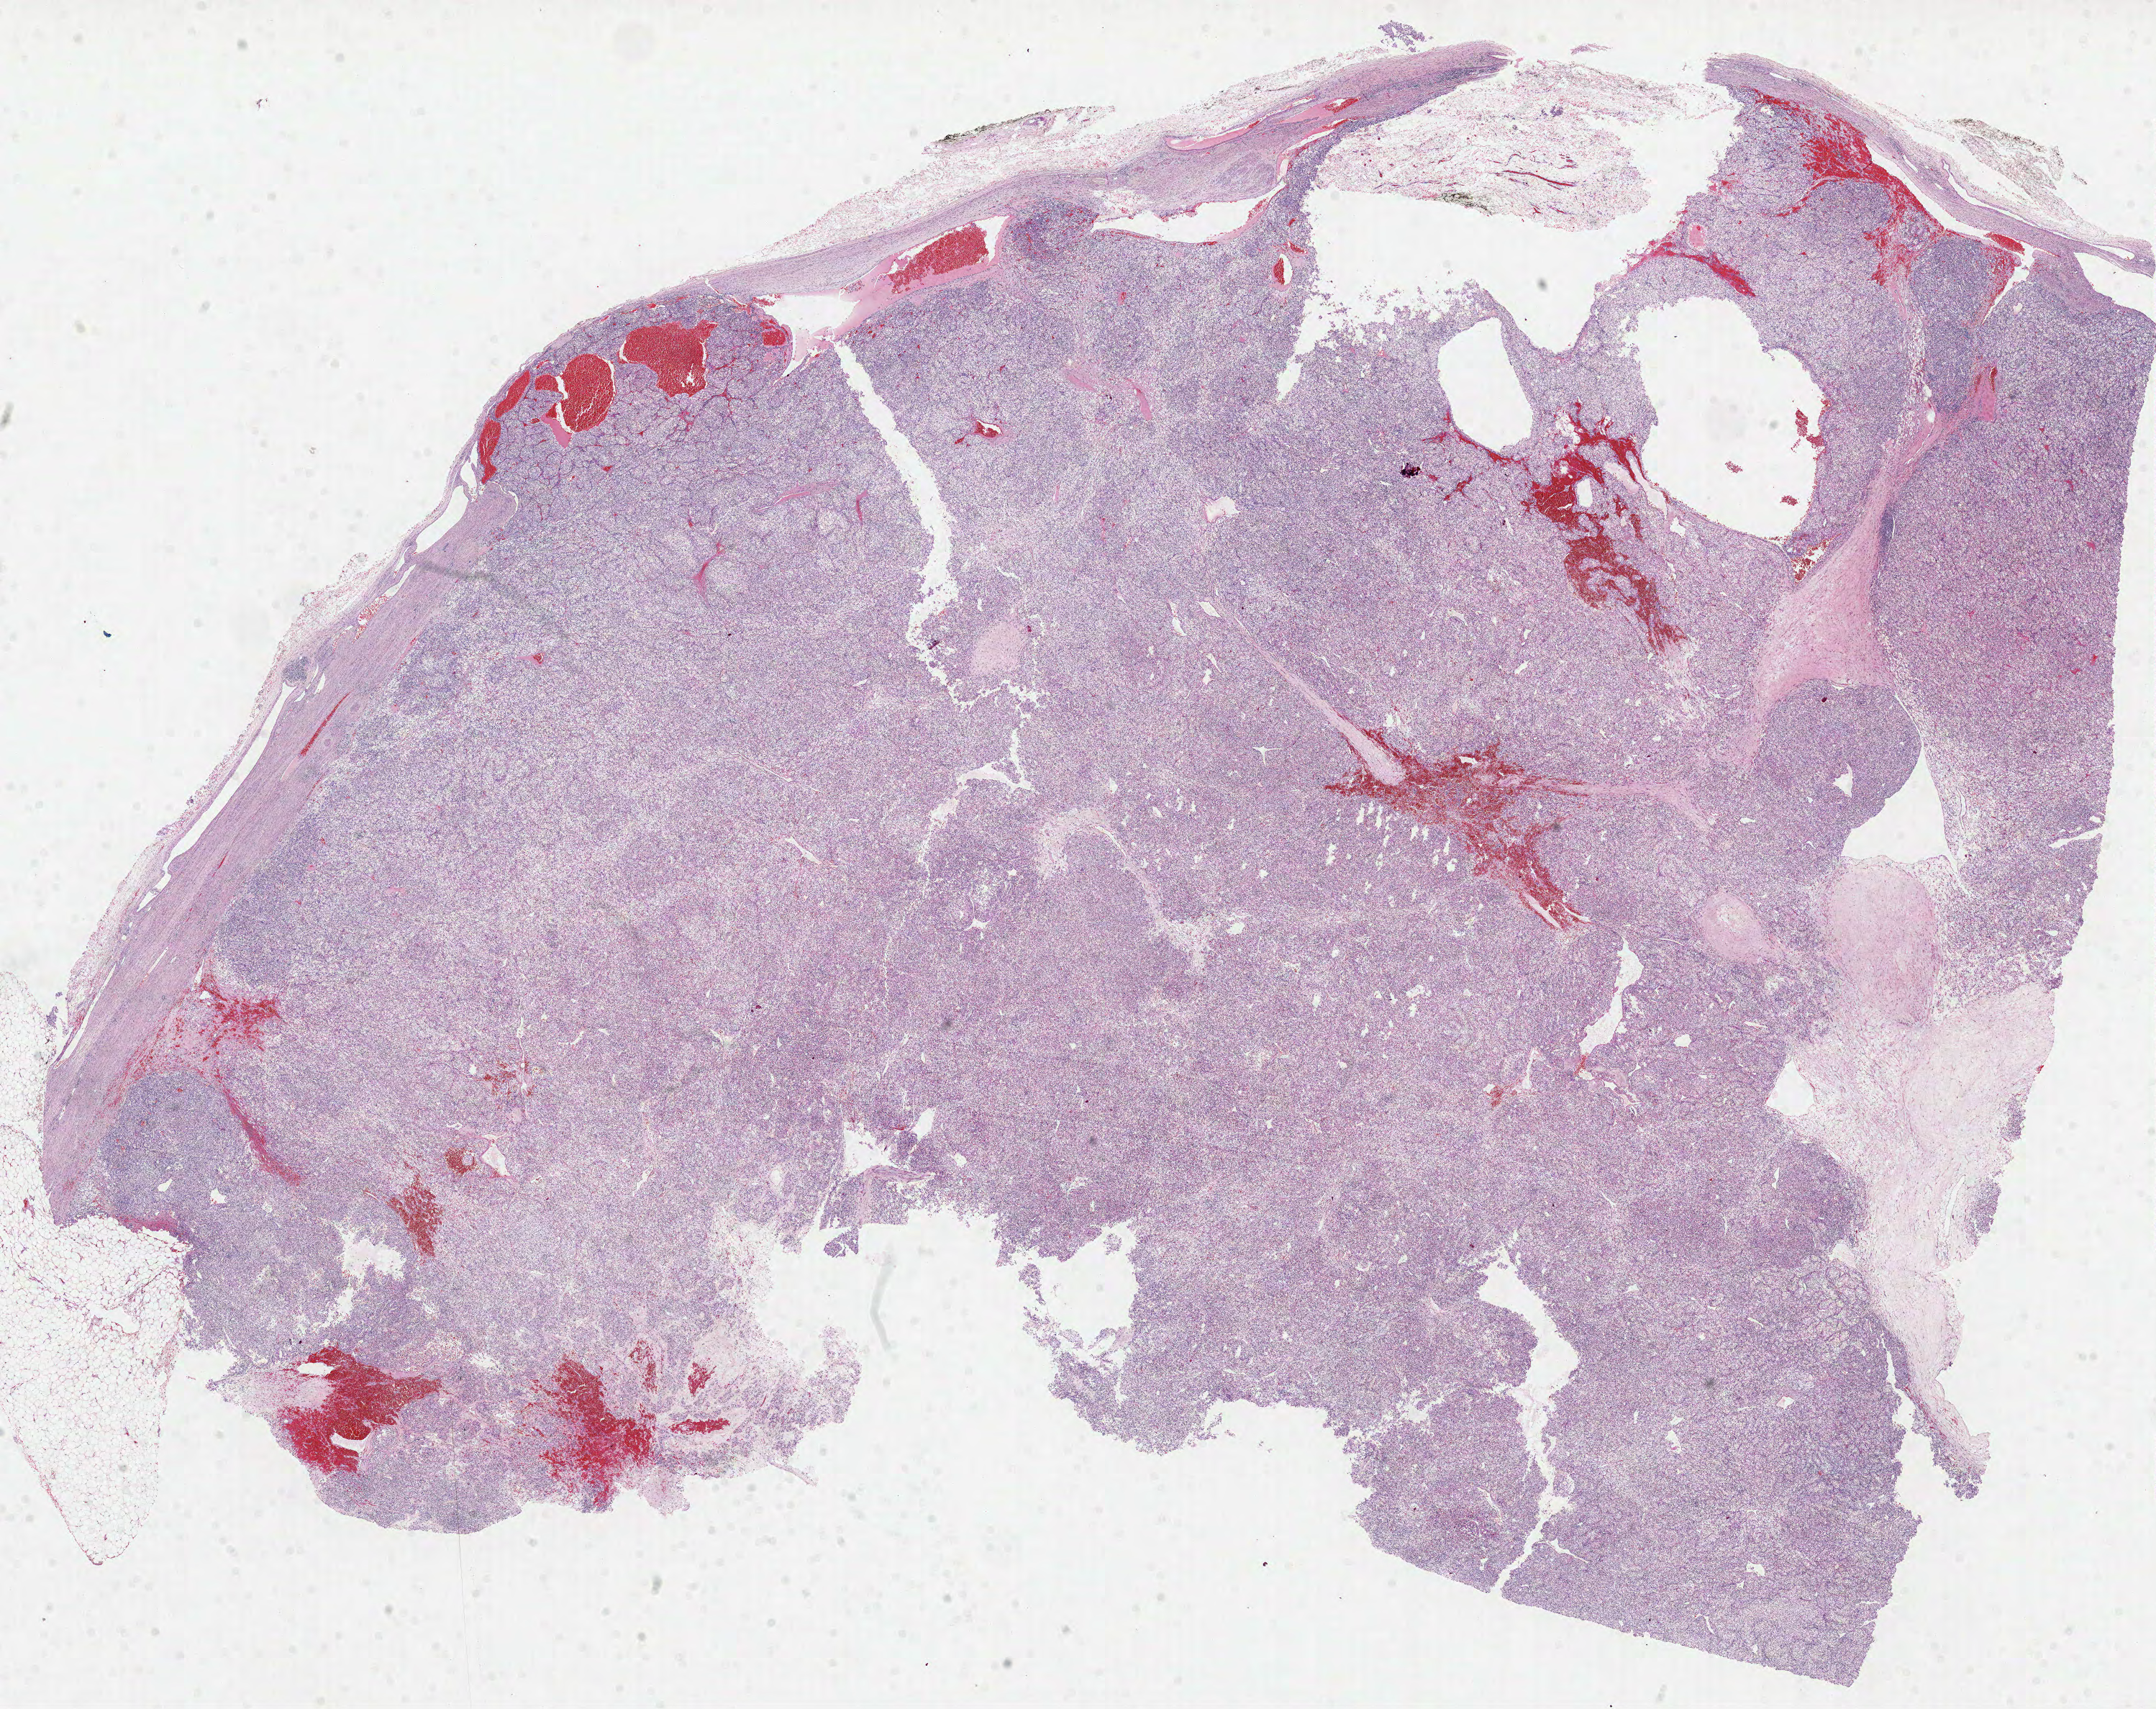
H&E whole-slide image — a low-resolution overview of the entire scanned area, about 24.2 x 19.2 mm, formalin-fixed paraffin-embedded (FFPE) diagnostic section, kidney, primary tumour sample. Female patient; age at initial diagnosis 69 years. Histologic grade: G3 (poorly differentiated).
* diagnosis: Clear cell adenocarcinoma, NOS
* TNM: T1b N0 M0
* AJCC pathologic stage: I